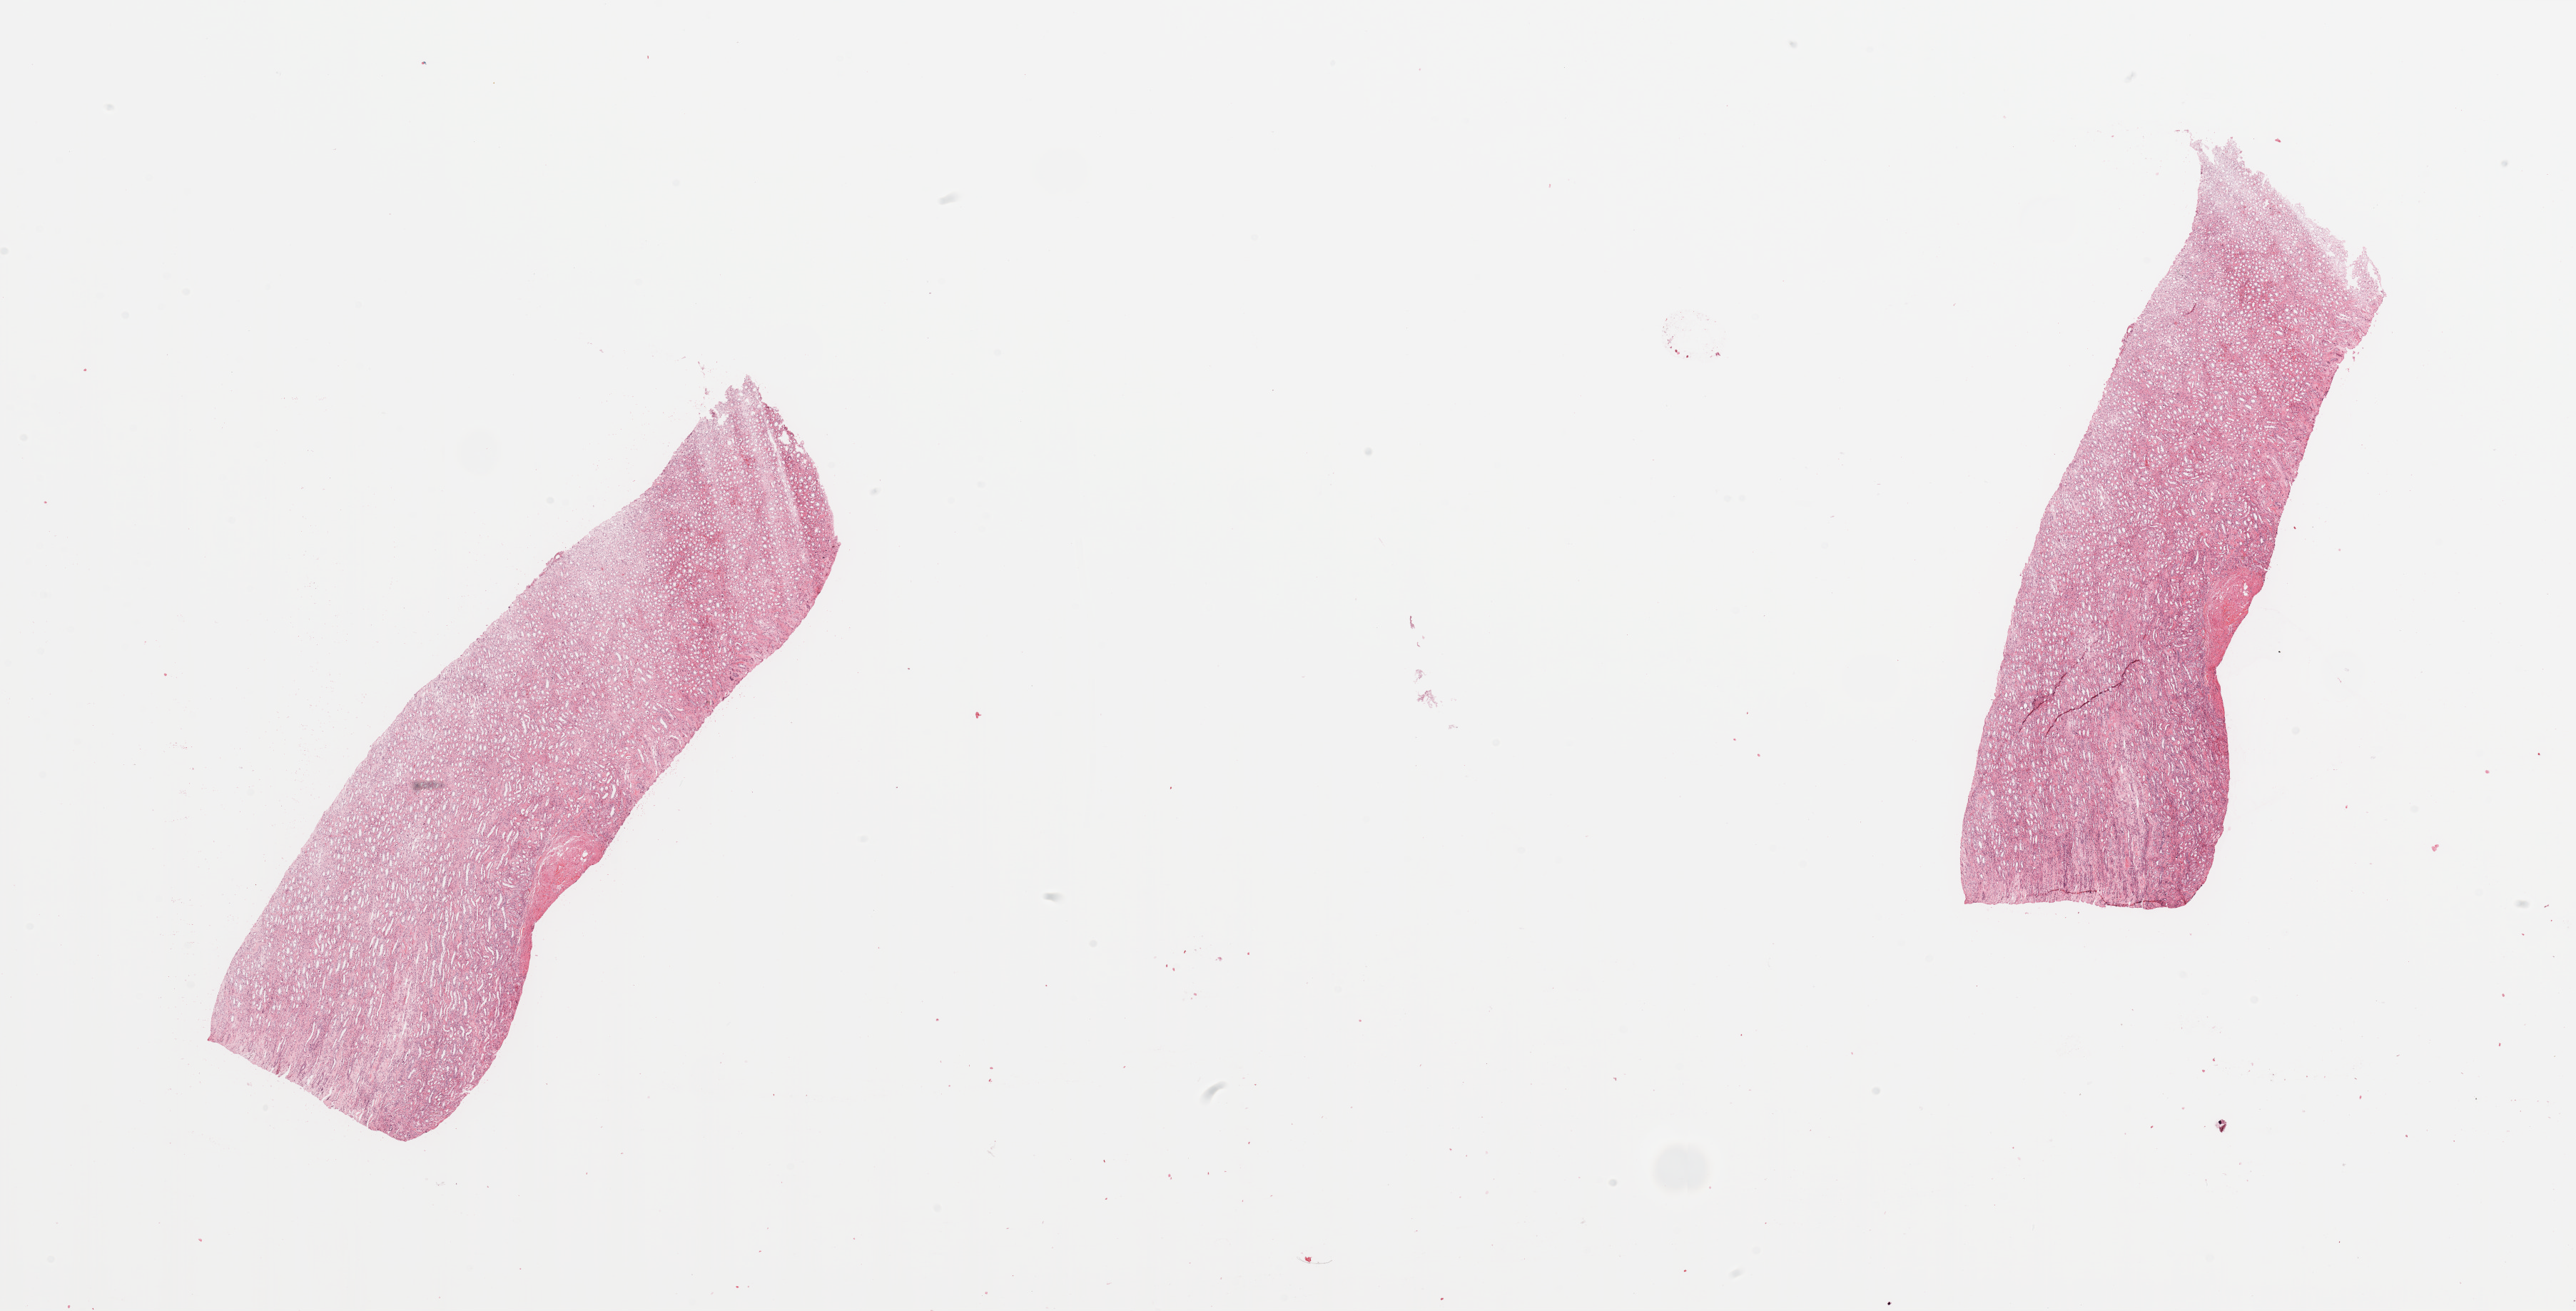
Whole-slide histology image, Hematoxylin and eosin (H&E) stained — low-resolution overview of the scanned area, about 28.5 x 14.5 mm. Kidney, normal (non-tumour) tissue. 57-year-old male patient.
- this section: normal (non-tumour) tissue from the same patient
- patient diagnosis: Renal cell carcinoma, NOS